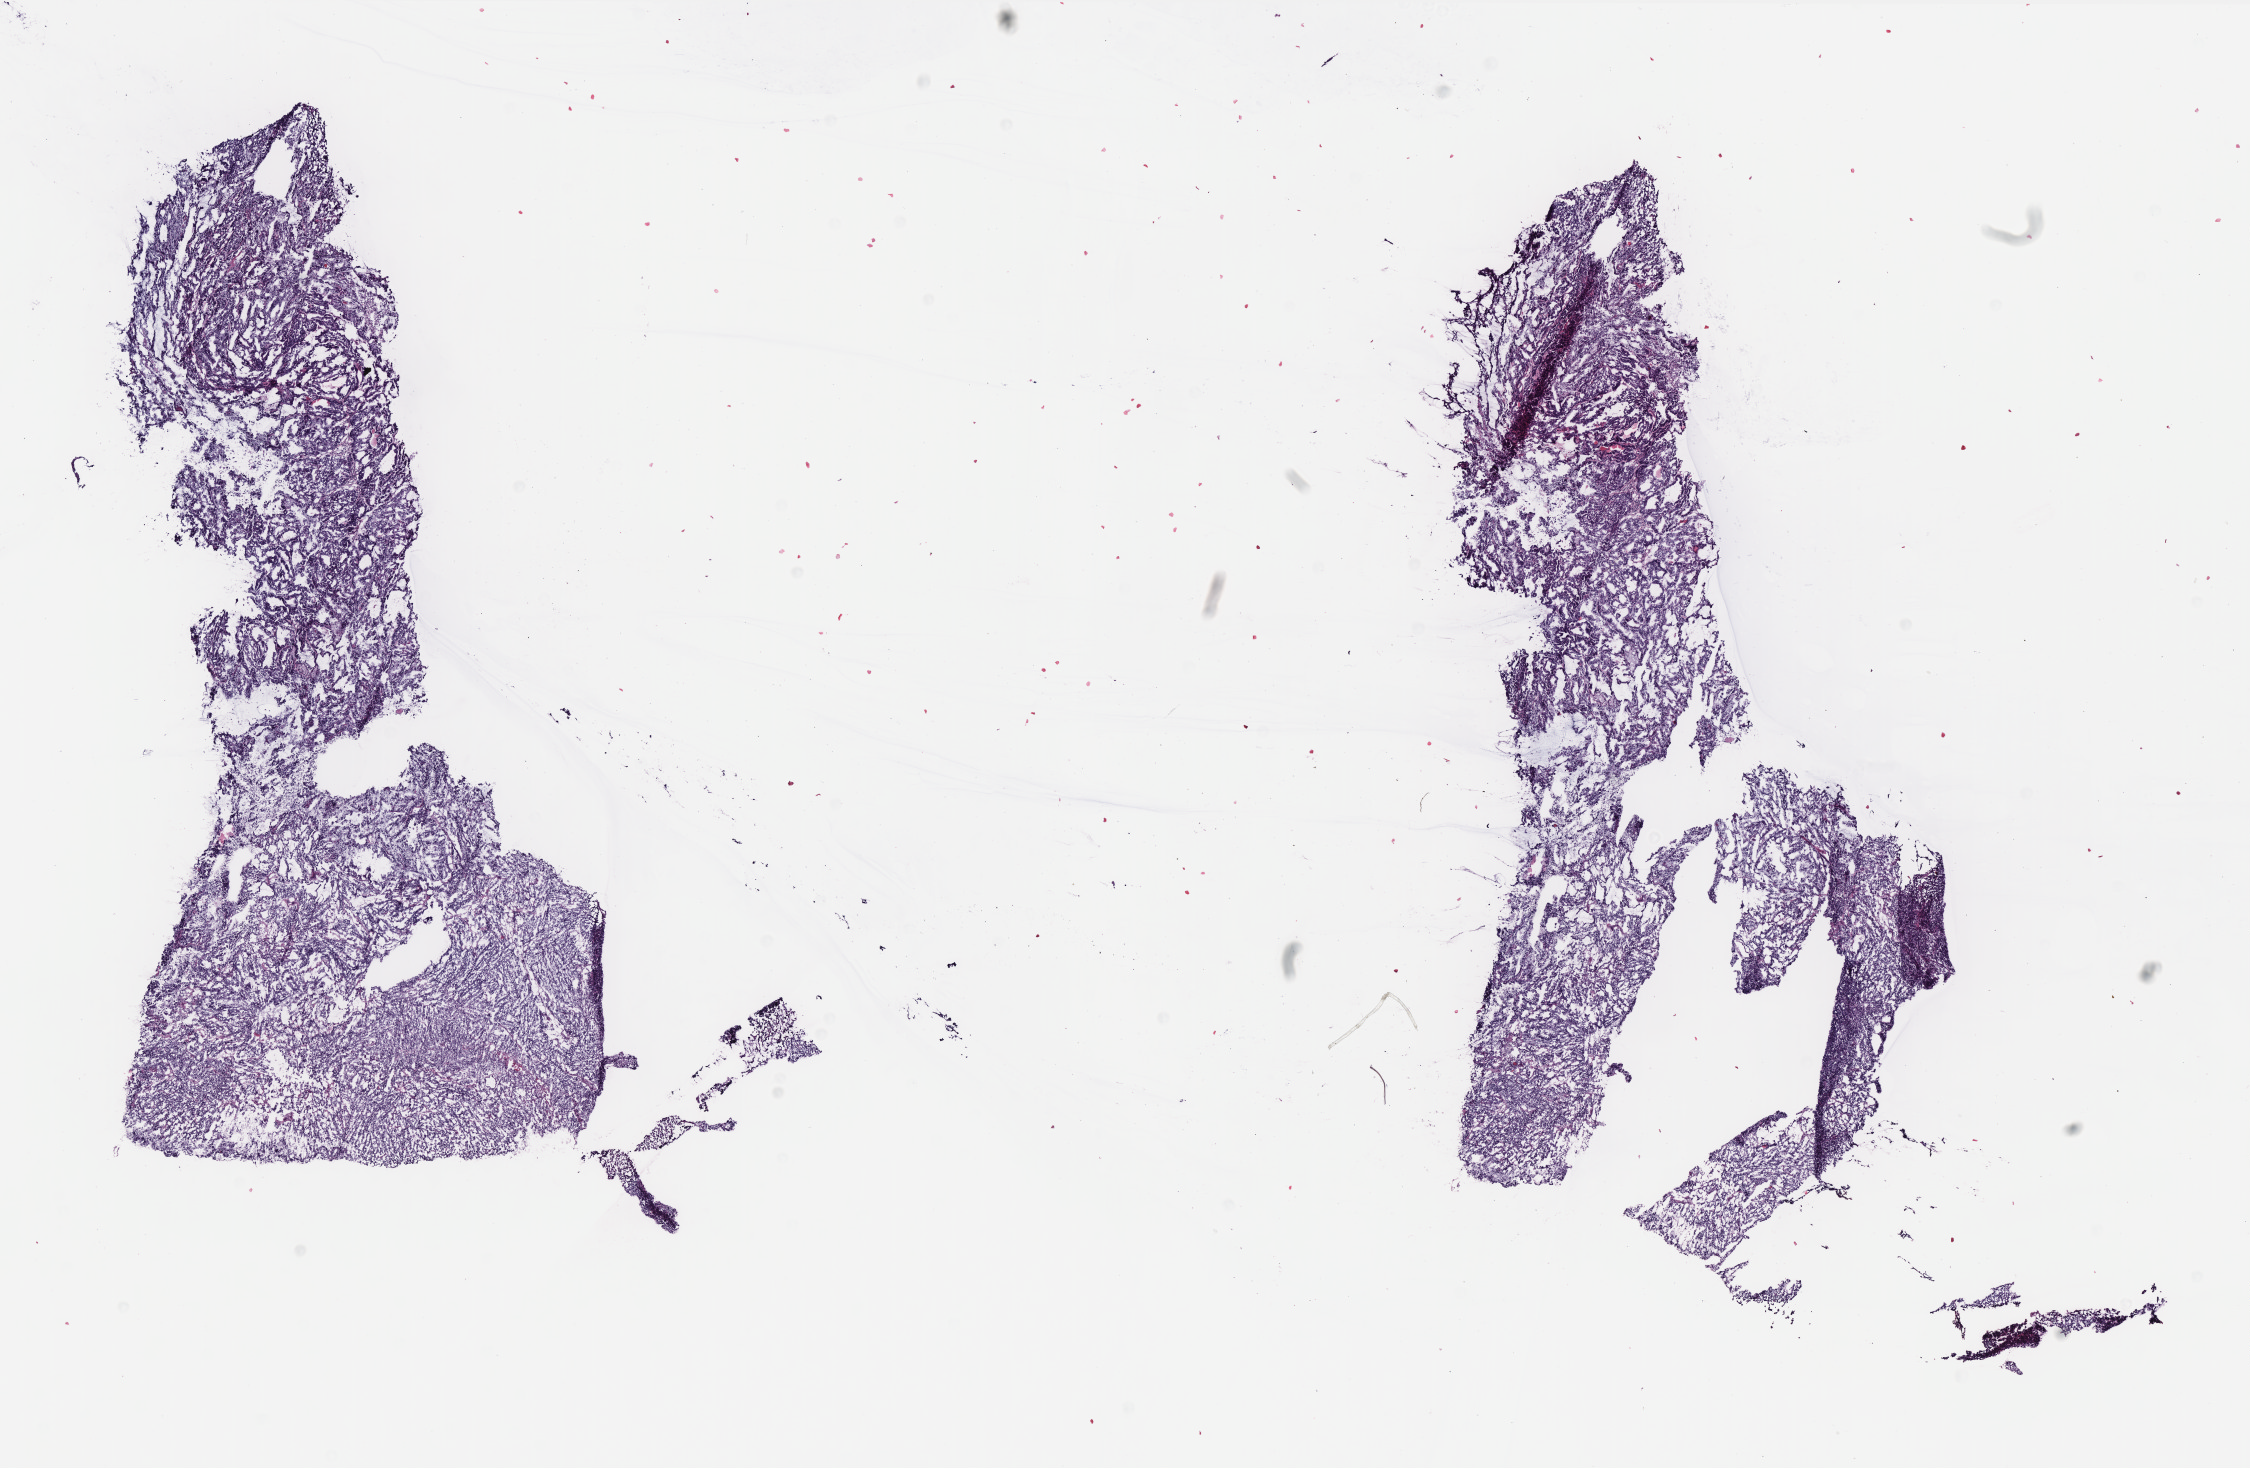
Whole-slide histology image, H&E, low-resolution overview of the scanned area, about 18.0 x 11.8 mm (from a 40x scan); frozen section from the top of the tissue portion; uterus, primary tumour sample. Patient: female, age at initial diagnosis 79 years. Histologic grade: G3 (poorly differentiated). Pathologist review of this section (percent, as recorded): tumour cells 100%, tumour nuclei 85%, normal cells 0%, stromal cells 0%, necrosis 0%. Infiltration values recorded for this section: lymphocyte infiltration 0%, monocyte infiltration 0%, neutrophil infiltration 0%.
- diagnosis: Endometrioid adenocarcinoma, NOS (endometrium)
- FIGO stage: IB